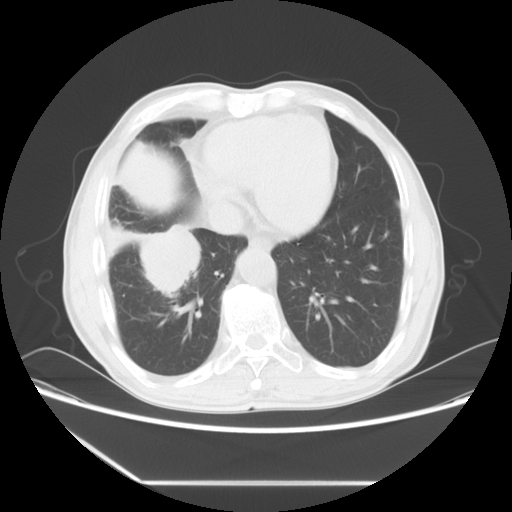
Chest CT, one axial slice; lung window (W 1500 / L -600 HU); 5 mm slice thickness; 512 × 512 image matrix, field of view 386 × 386 mm. Patient: male, 72 years. Case-level facts recorded for this patient, not image findings: clinical TNM (as recorded): T1c N0 M0.
Outlined on this slice (rectangle marked by the reading radiologist):
- lung tumour (recorded histology: squamous cell carcinoma): bounding box <103,218,216,308> (left, top, right, bottom; pixels)